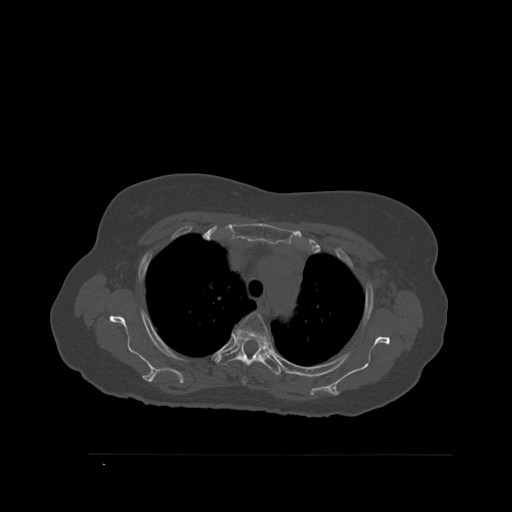
CT including the spine, one axial slice. Position 413 of 527 along the scan axis. Bone window (W 1800 / L 400 HU). 1.5 mm slice thickness. 512 × 512 image matrix, field of view 470 × 470 mm. Female patient, age 73 years. Case-level facts recorded for this patient, not image findings: primary cancer: breast; vertebrae with lytic lesions (as recorded): L2.
Annotated regions visible in this slice (semi-automatic segmentation, software-assisted and operator-edited):
- T3 vertebra: bounding box <236,313,270,383> (left, top, right, bottom; pixels)
- T4 vertebra: <217,334,281,375>